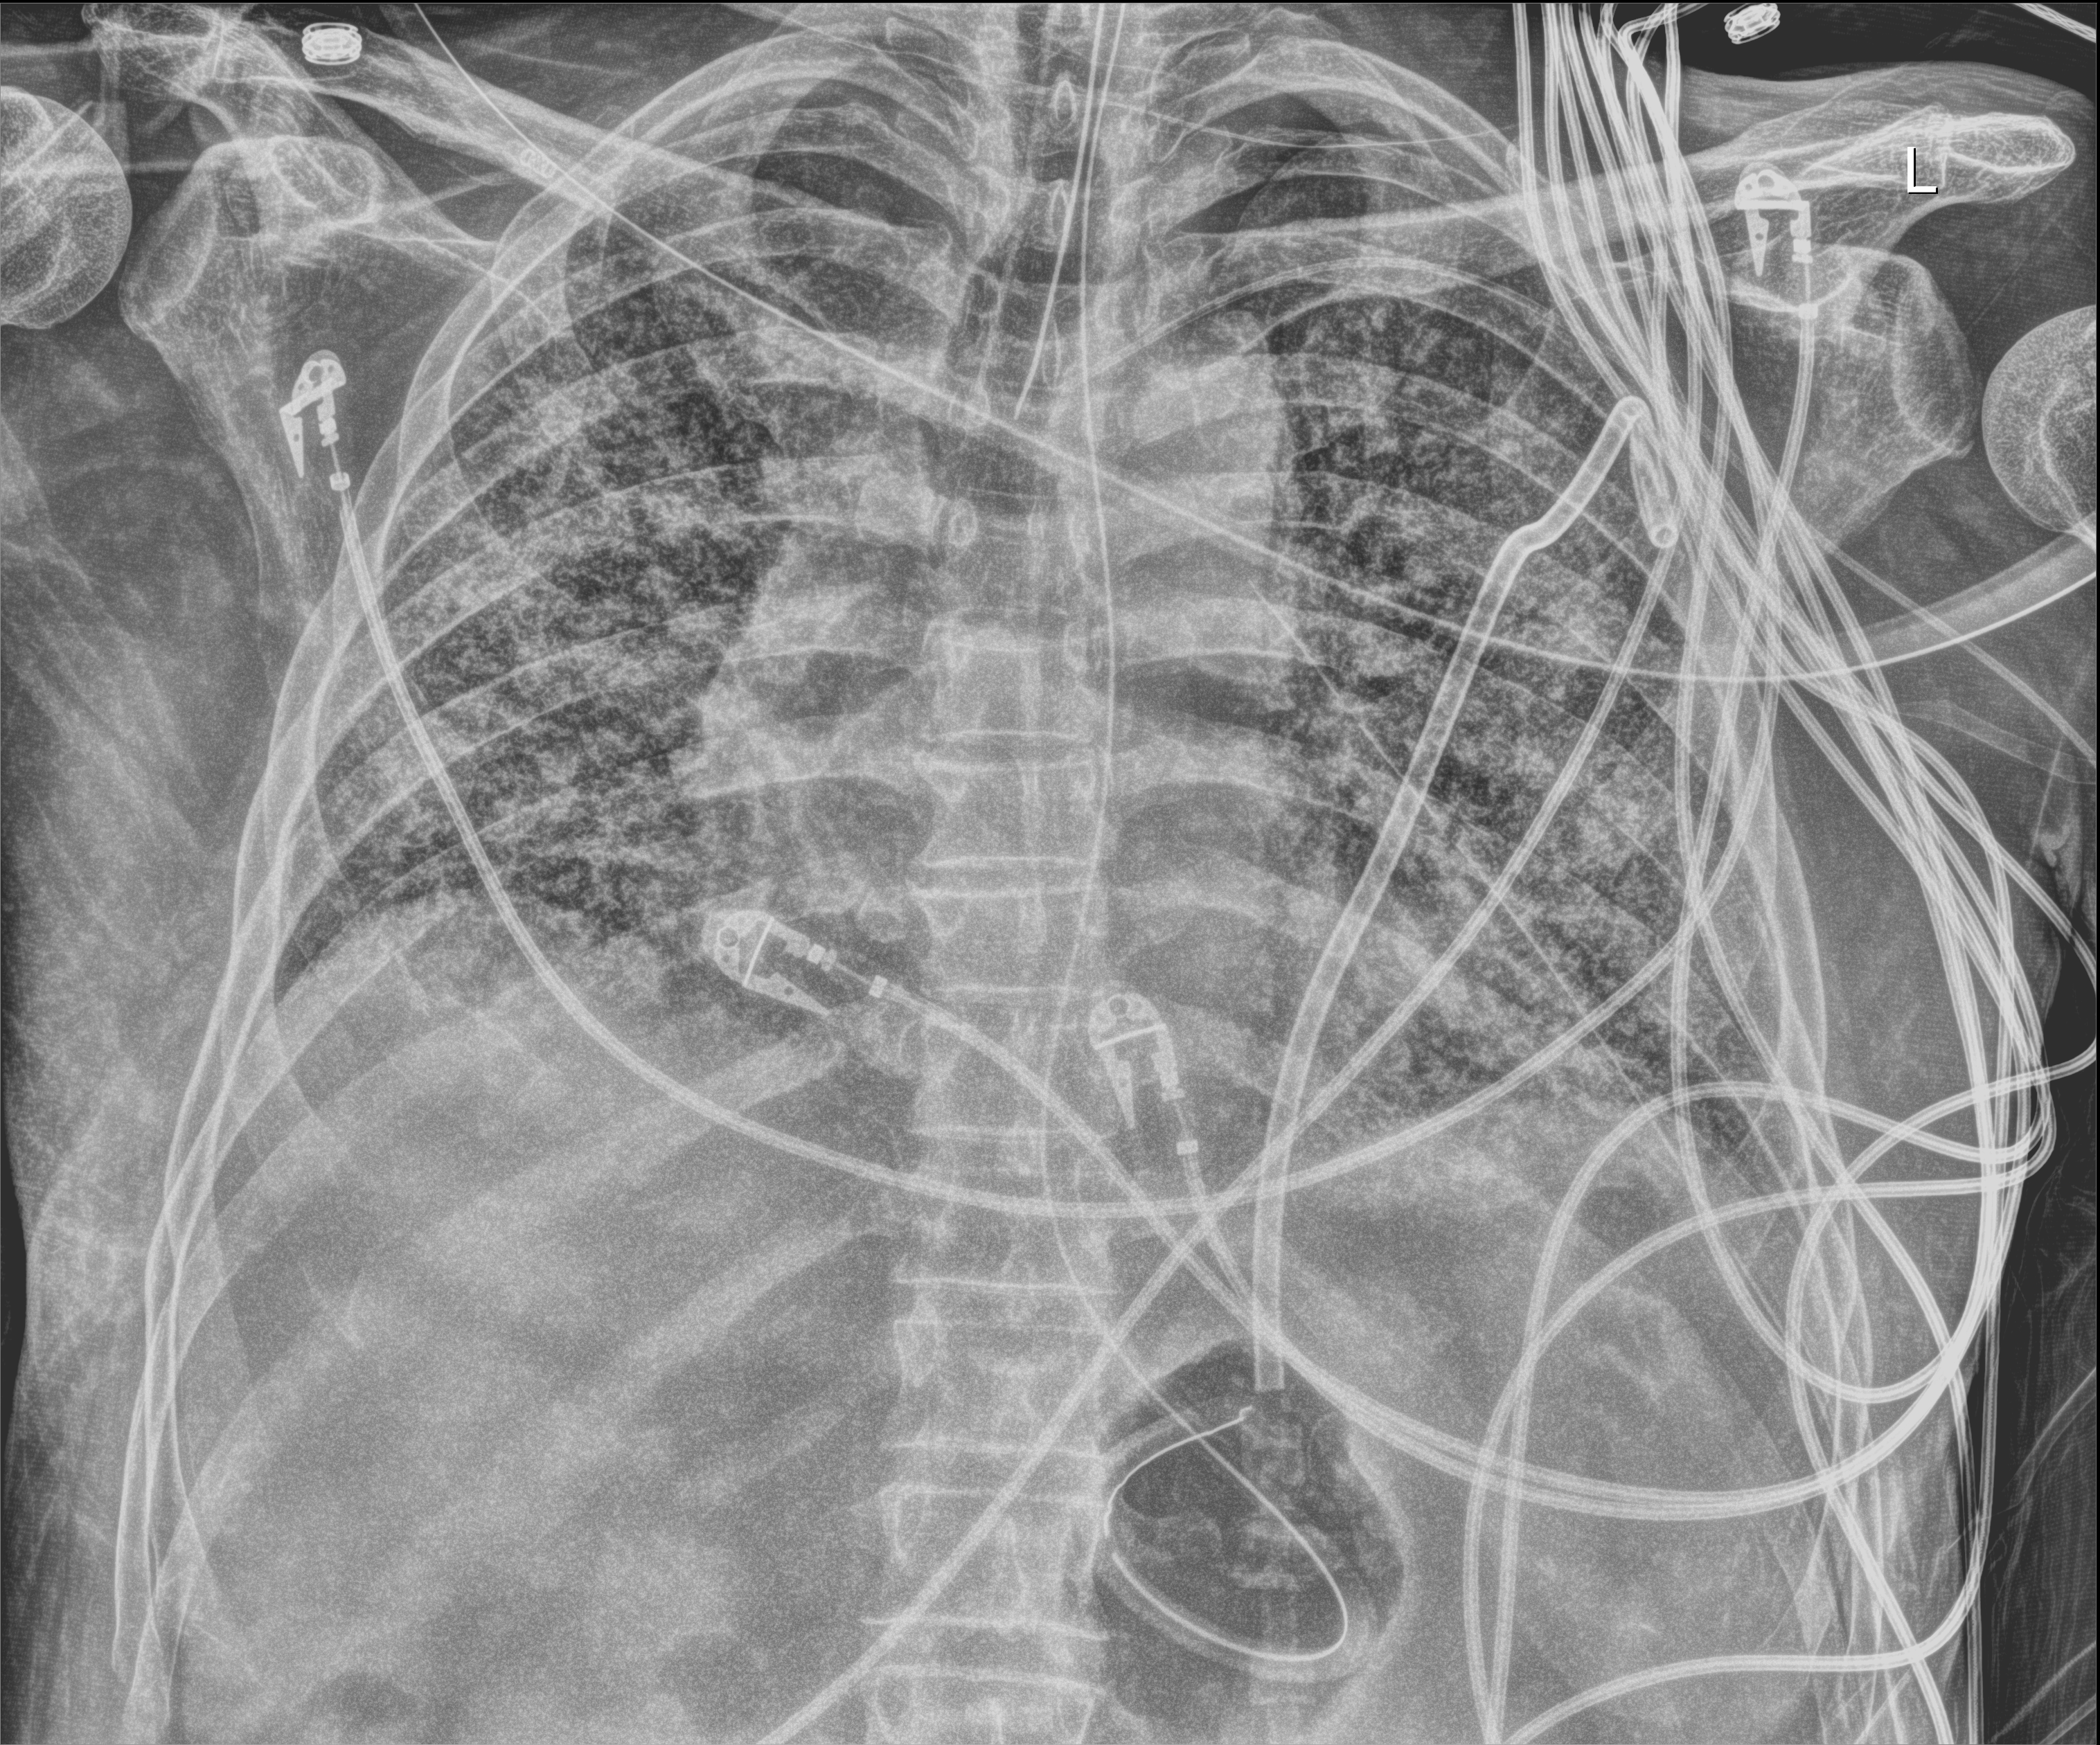
Chest radiograph; anteroposterior (AP) projection. Patient hospitalised with COVID-19; male, aged 60–74 years.
From the hospital-stay record, not from the radiograph (when in the stay this image was taken is not recorded): admitted to intensive care during this hospital stay: yes; mechanically ventilated during this hospital stay: yes.